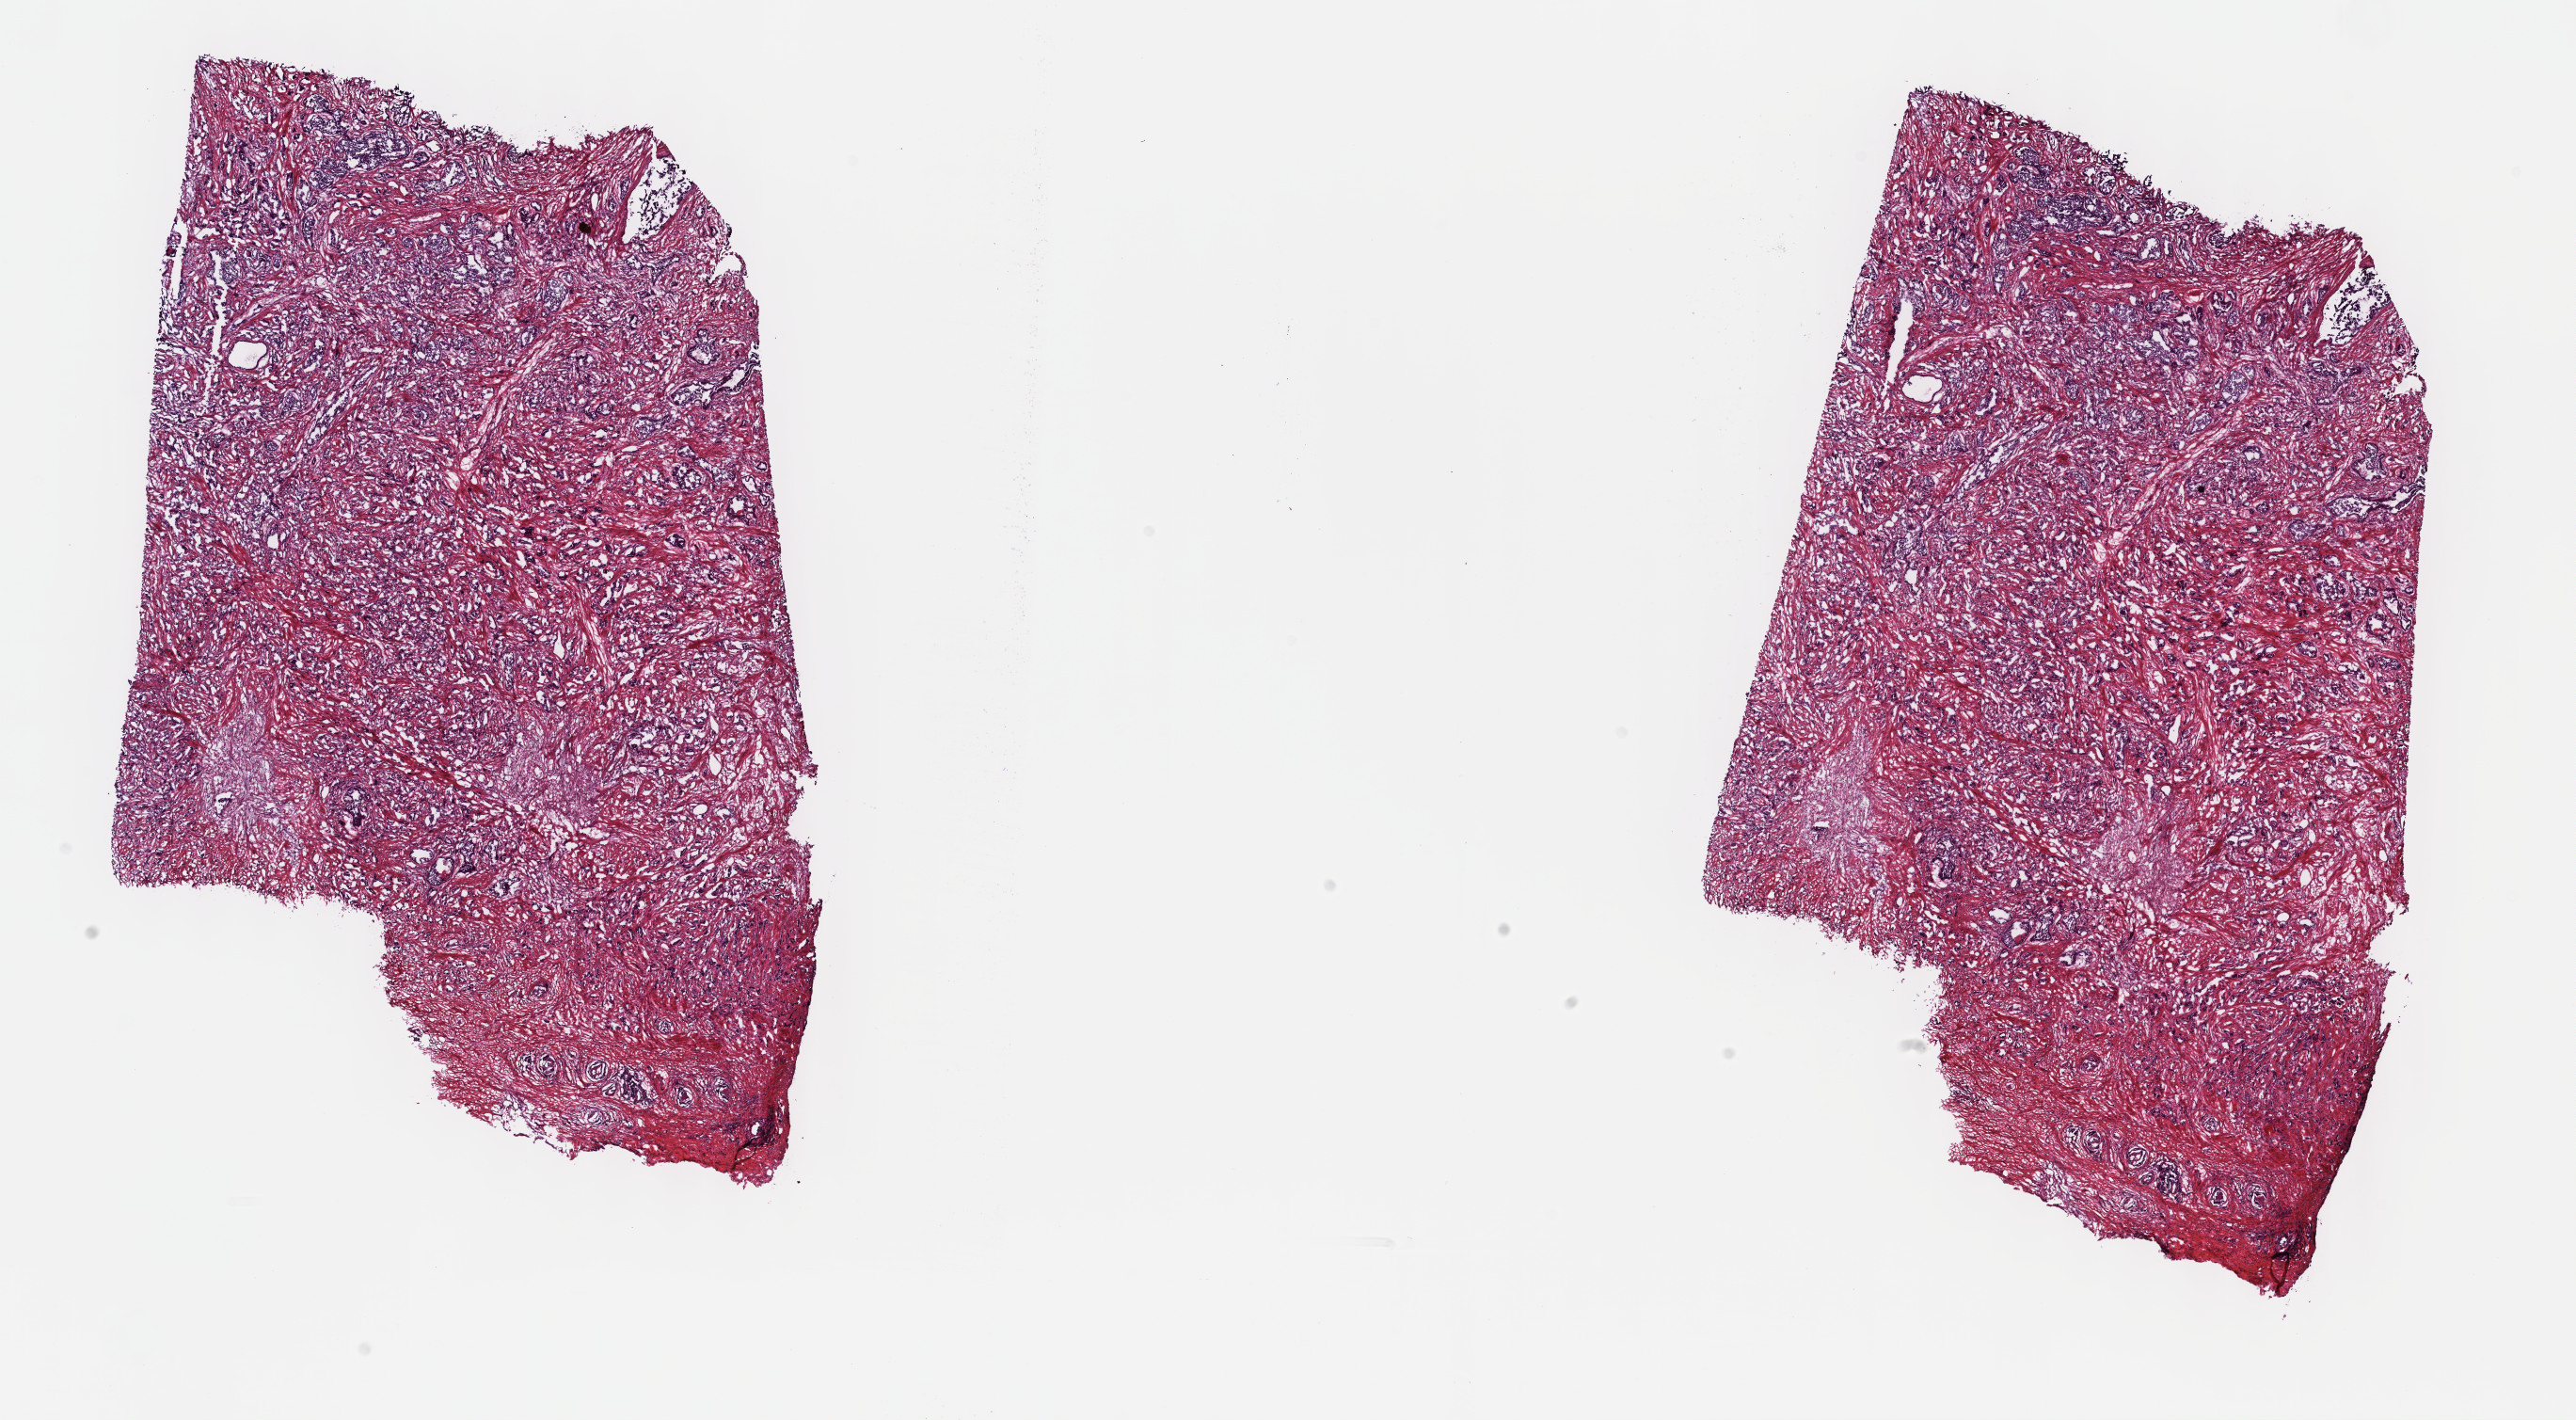
Digitized Hematoxylin and eosin (H&E) stained tissue section (whole slide) — shown as a low-resolution overview of the whole scanned area (about 22.1 x 12.2 mm, from a 40x scan), frozen section from the top of the tissue portion, sample: primary tumour, prostate. Patient: male, age at initial diagnosis 66 years. Gleason score: 9 (4+5). Composition of this section per pathologist review: tumour cells 70%, tumour nuclei 80%, normal cells 0%, stromal cells 30%, necrosis 0%. Inflammatory infiltration, as recorded: lymphocyte infiltration 0%, monocyte infiltration 0%, neutrophil infiltration 0%.
- lymph nodes positive (case pathology): 0 of 5 examined
- laterality: bilateral
- histologic diagnosis: Adenocarcinoma, NOS (prostate gland)